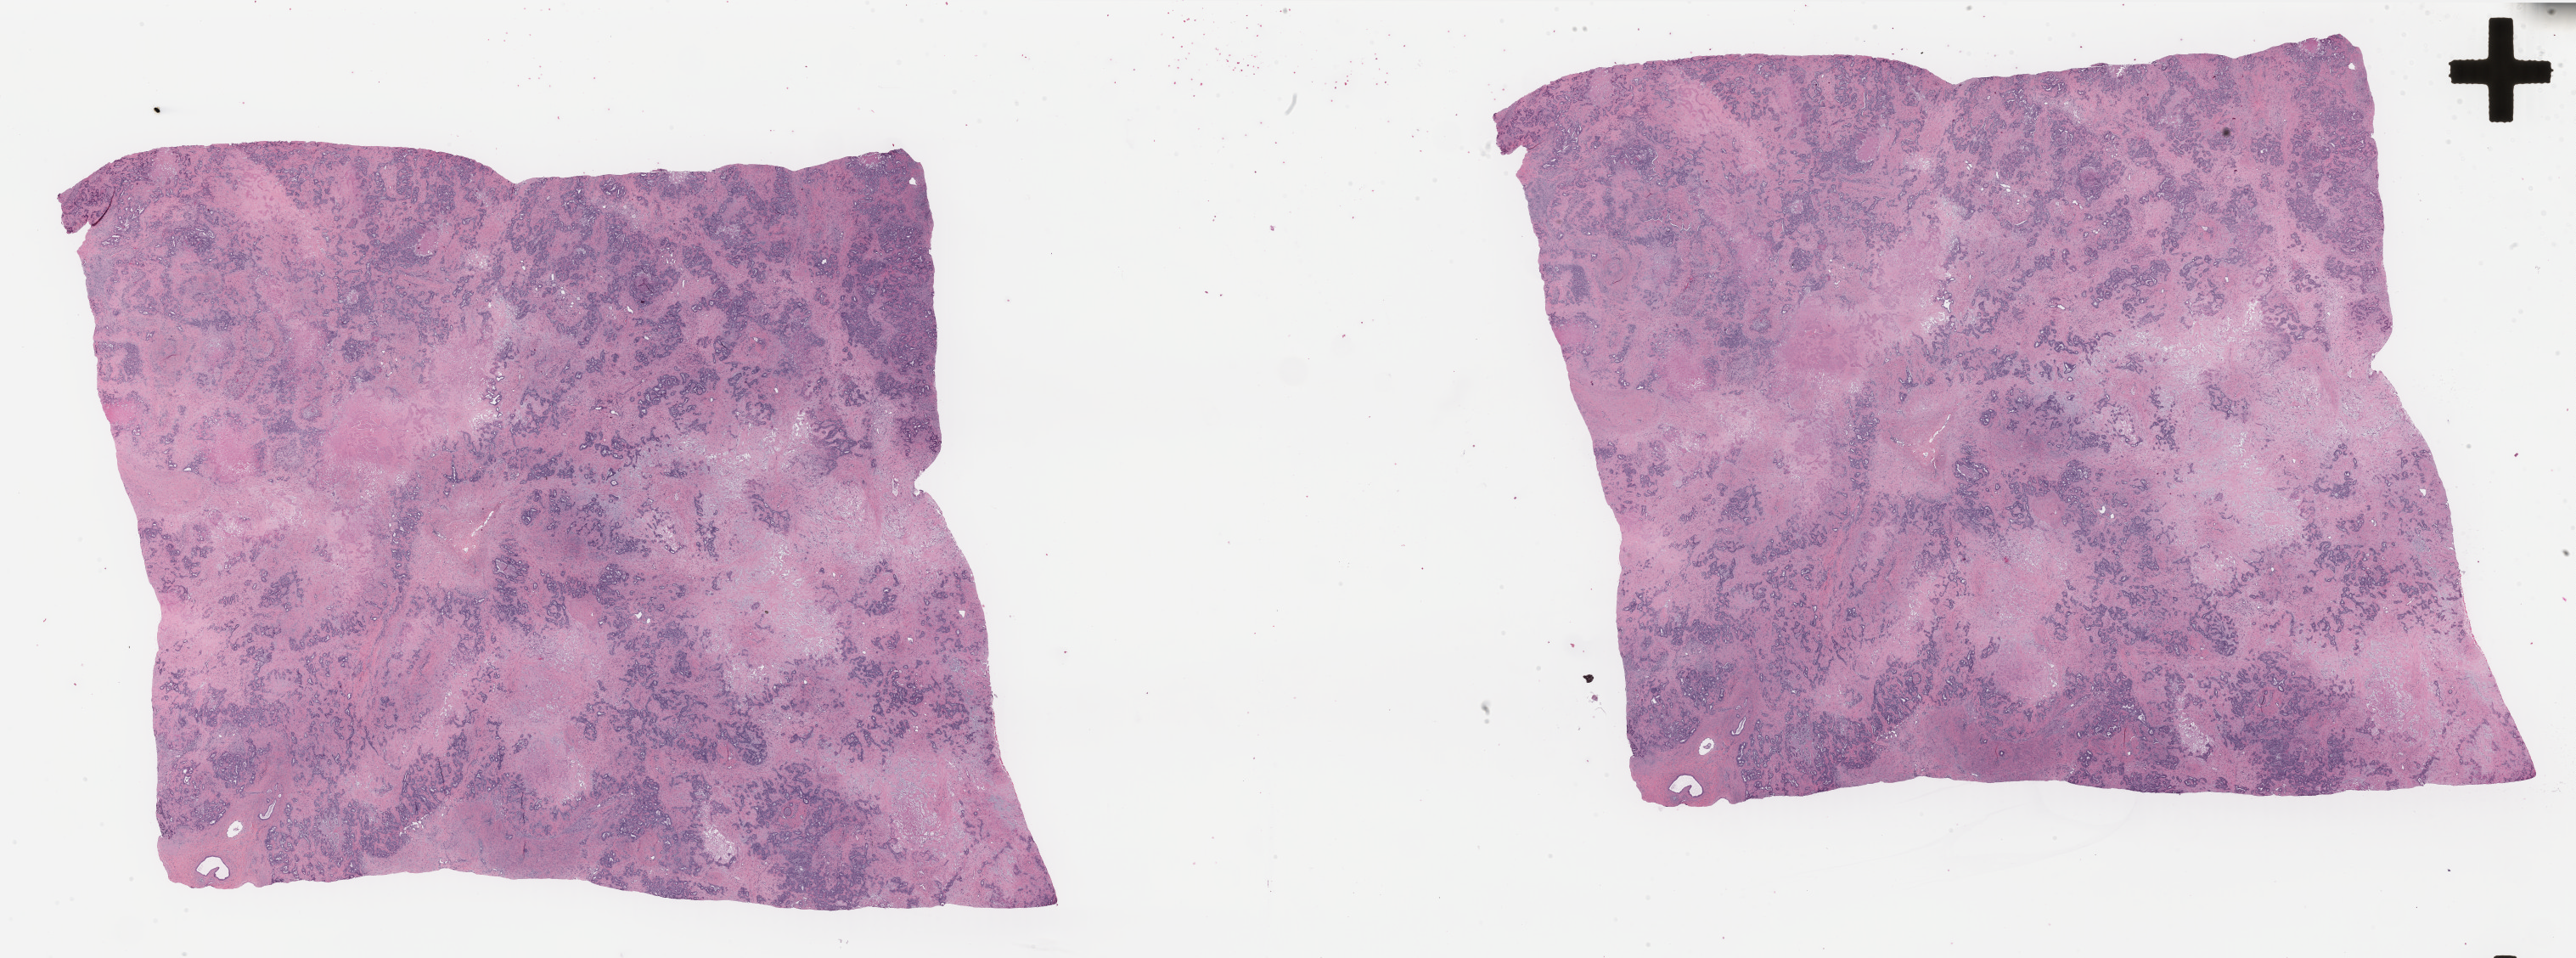
H&E-stained whole-slide image — whole scanned area (about 48.0 x 17.8 mm) shown as a low-resolution overview, FFPE section, bile duct, primary tumour sample. Patient: female, age at initial diagnosis 74 years. Histologic grade: G2 (moderately differentiated).
Histologic diagnosis: Cholangiocarcinoma (intrahepatic bile duct). AJCC pathologic stage: IVA (7th edition).